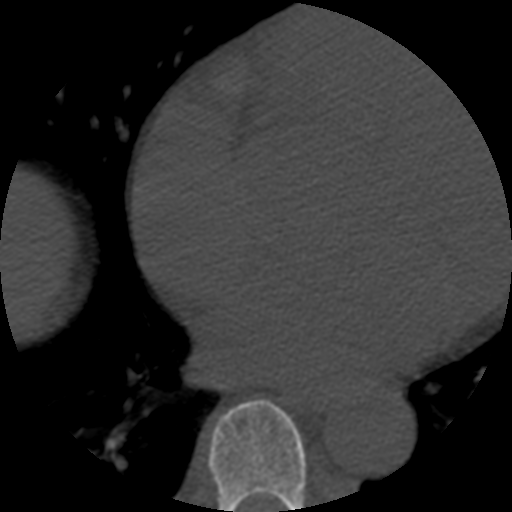
CT including the spine, one axial slice; position 334 of 508 along the scan axis; bone window (W 1800 / L 400 HU); 1.25 mm slice thickness; 512 × 512 image matrix. Patient age 57 years. Case-level facts recorded for this patient, not image findings: primary cancer: prostate.
Outlined on this slice (semi-automatic segmentation, software-assisted and operator-edited):
- T7 vertebra: bounding box [x1, y1, x2, y2] px = [208, 400, 307, 512]